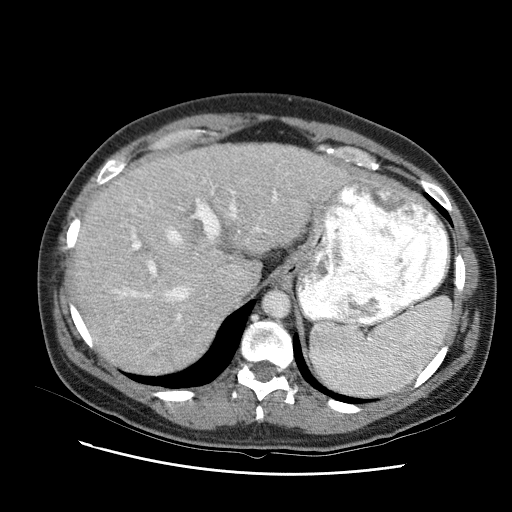
Contrast-enhanced abdominal CT (liver protocol), one axial slice; position 70 of 95 along the scan axis; reconstruction kernel STANDARD; 120 kVp; one of 2 acquisitions stored at this slice position; soft-tissue window (W 400 / L 40 HU); 2.5 mm slice thickness; 512 × 512 image matrix, field of view 360 × 360 mm. From the clinical record (not read from this slice): diagnosis: hepatocellular carcinoma (patient treated with transarterial chemoembolisation; whether this scan precedes or follows treatment is not stated here); TNM stage (as recorded): Stage-I; Child-Pugh class: B; tumour nodularity: uninodular.
Annotated regions visible in this slice (semi-automatically segmented with operator editing):
- liver parenchyma outside the tumour (the mass and vessels are separate outlines, so this box may not span the whole liver): box from (x=70, y=140) to (x=356, y=360) px
- liver vessels: (x=100, y=182)–(x=312, y=331)